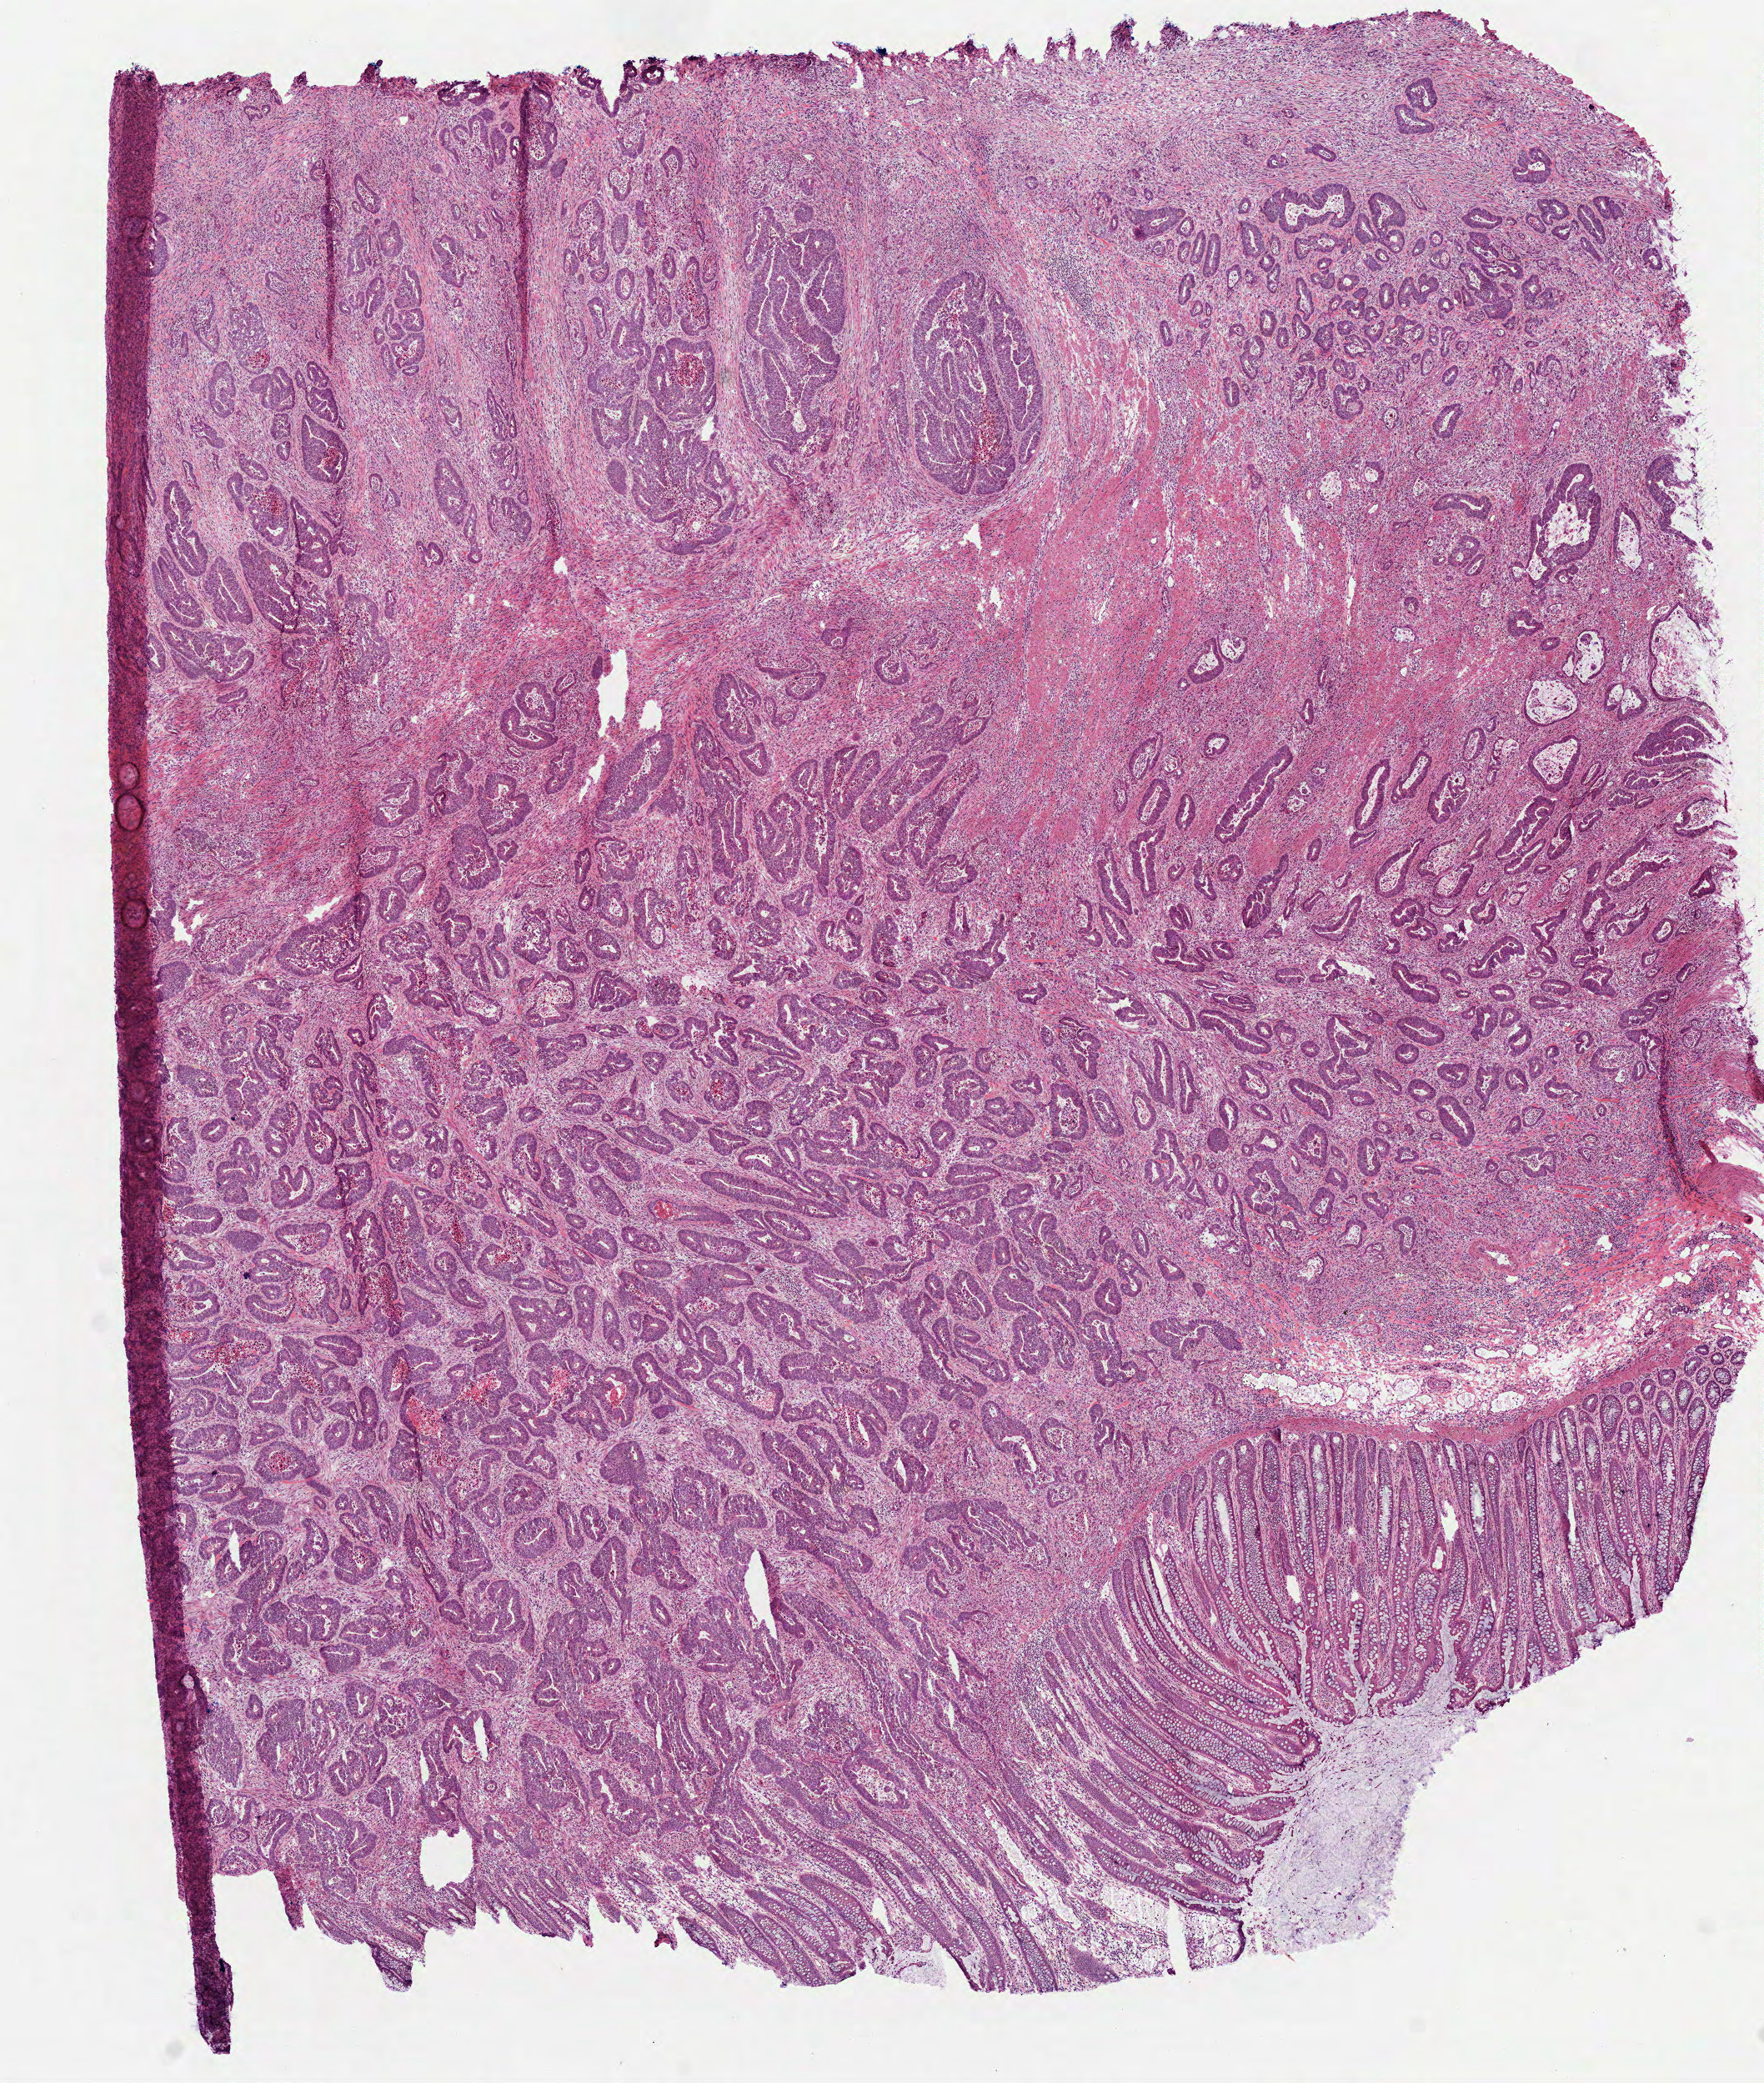
Hematoxylin and eosin (H&E) stained whole-slide image, low-resolution overview of the scanned area, about 8.5 x 10.1 mm (slide scanned at 40x), frozen section, sample: primary tumour, colon. Female patient; age at initial diagnosis 65 years. Slide review estimates, as recorded: tumour cells 70%, tumour nuclei 70%, normal cells 15%, stromal cells 0%, necrosis 15%. Infiltration values recorded for this section: lymphocyte infiltration 10%, monocyte infiltration 2%, neutrophil infiltration 10%.
• pathologic diagnosis: Adenocarcinoma, NOS
• lymph nodes positive (case pathology): 1 of 65 examined
• AJCC pathologic stage: IIIB (7th edition)